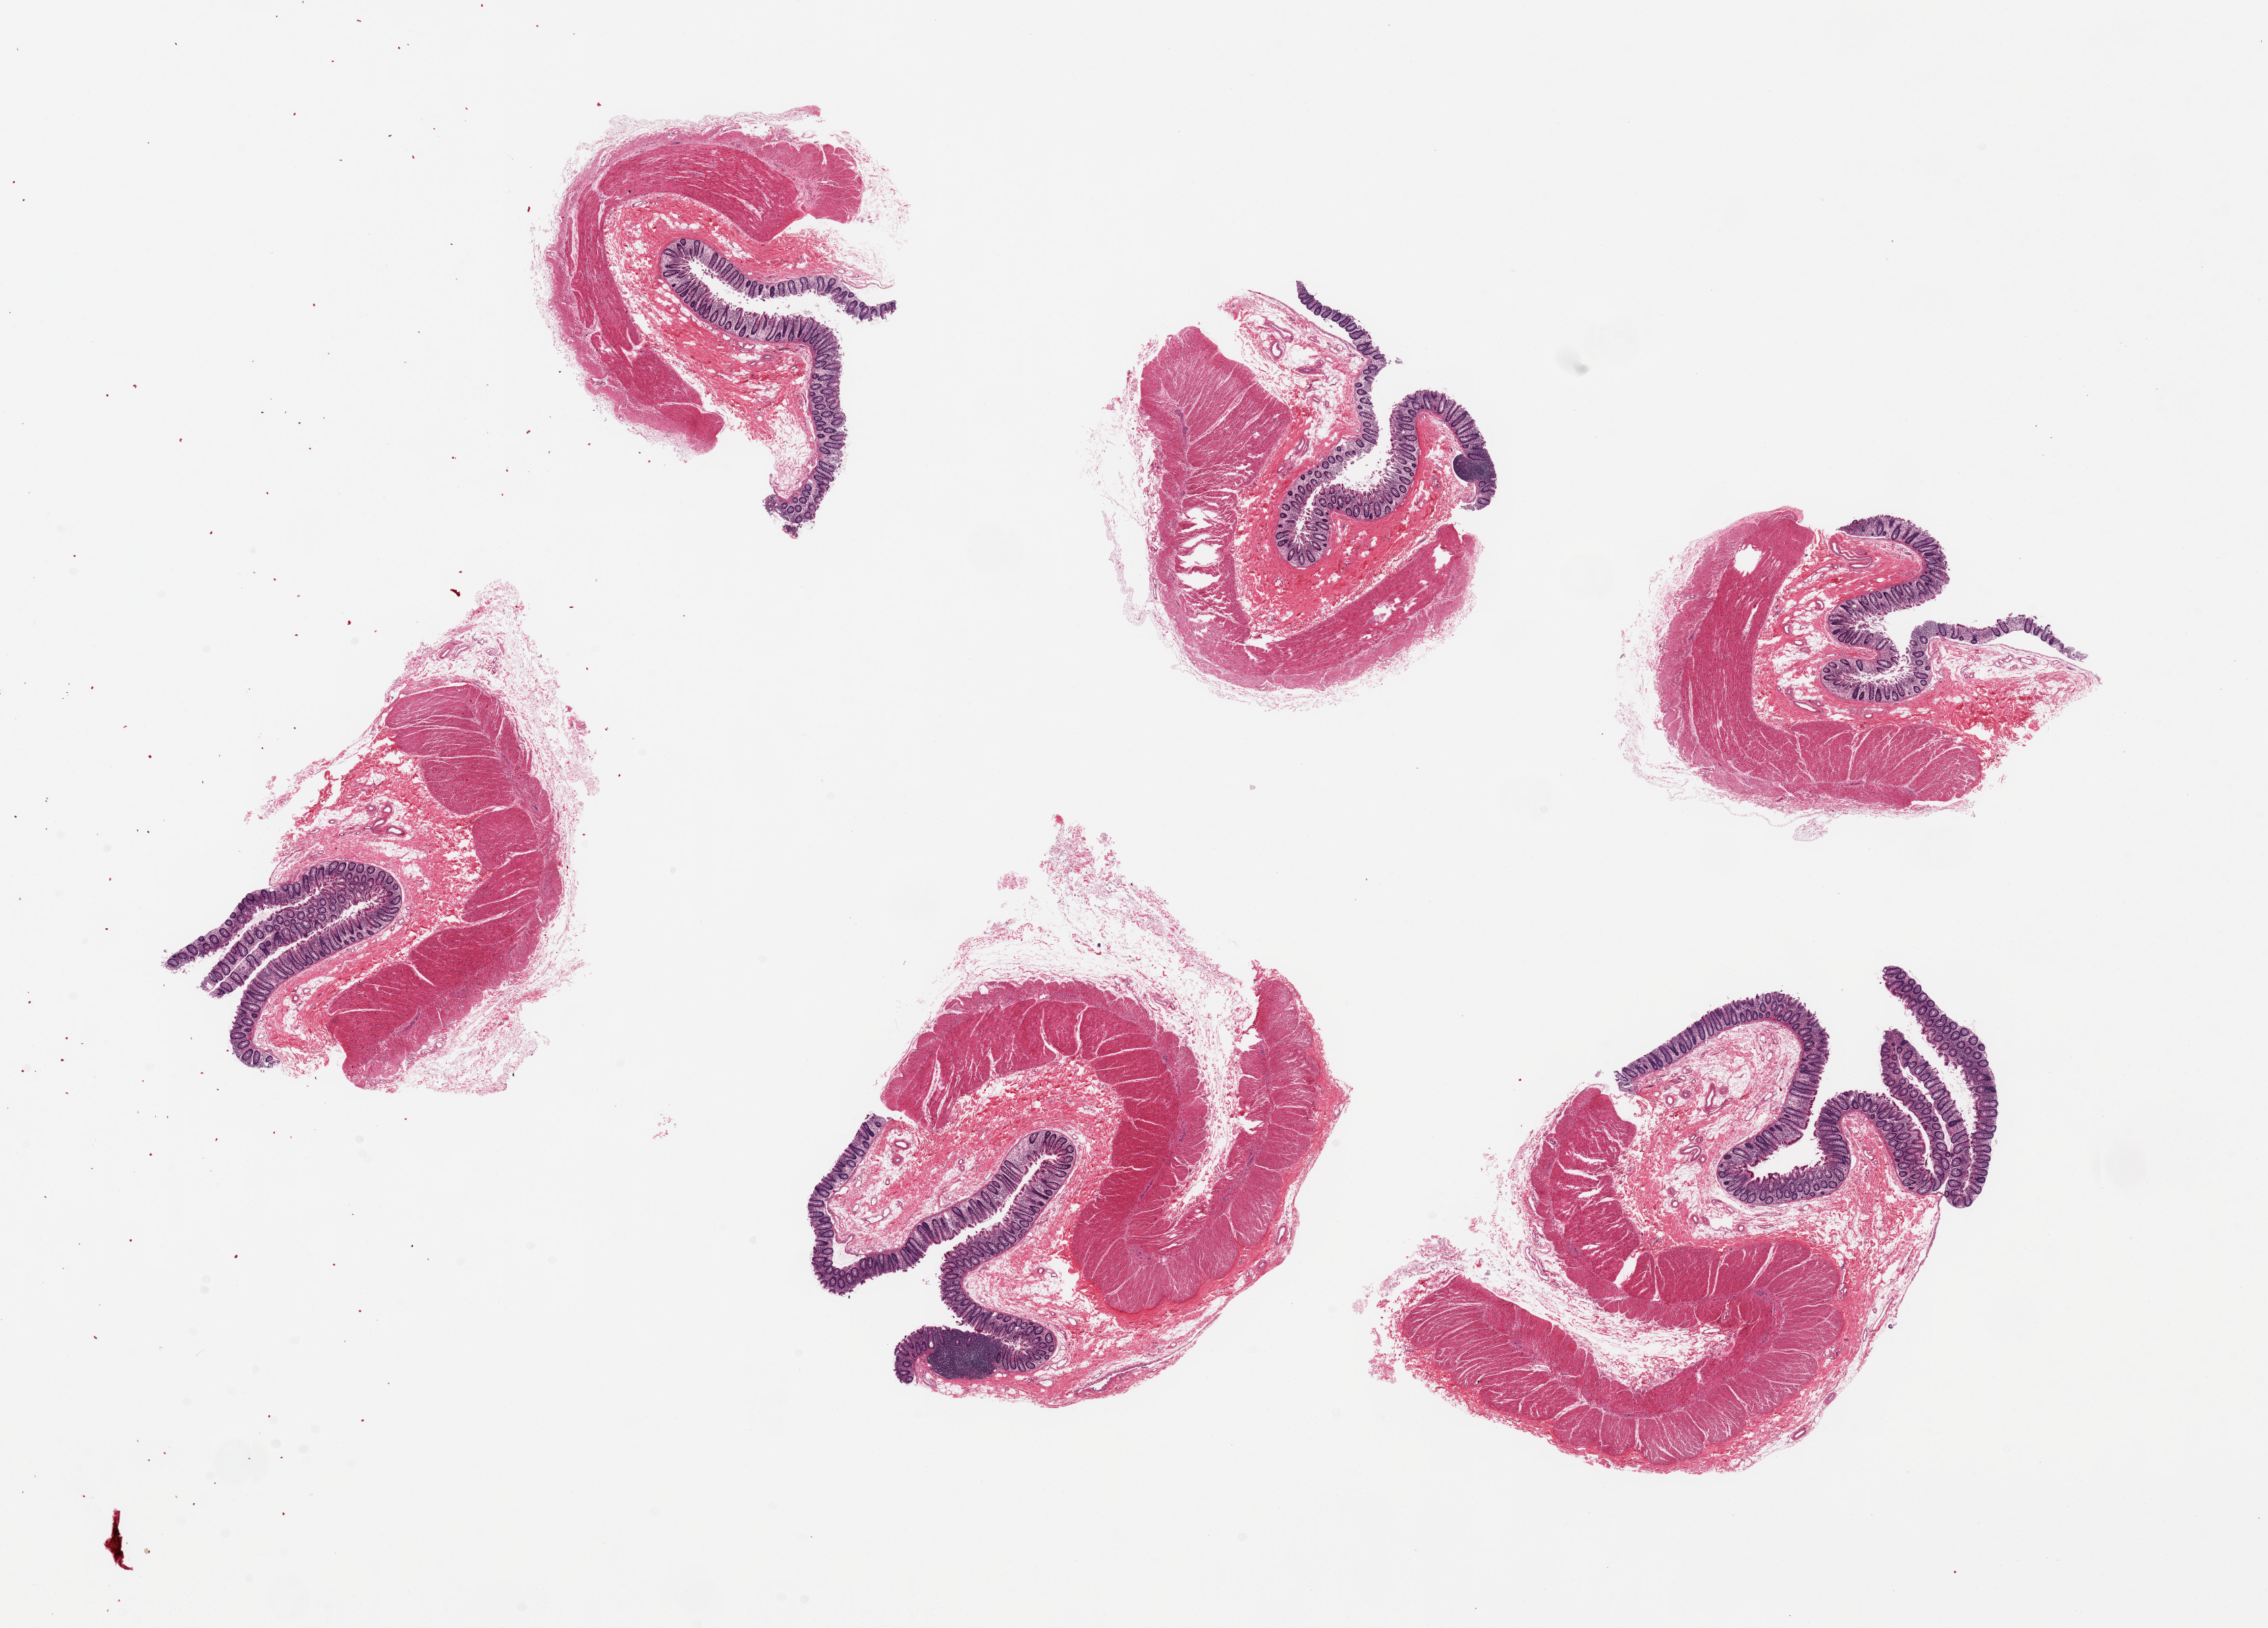
Hematoxylin and eosin (H&E) whole-slide image, a low-resolution overview of the entire scanned area, about 26.6 x 19.1 mm; PAXgene-fixed, paraffin-embedded tissue; target tissue: transverse colon; donor tissue sample. Donor sex: female.
Review note (as recorded): 6 pieces up to 7.6x8.7 mm; surface partially sloughed.